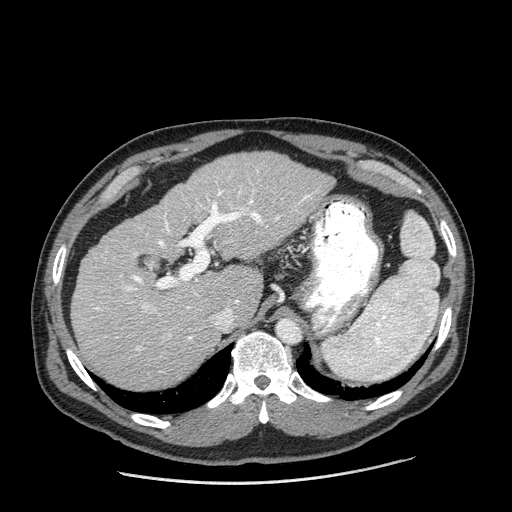
Contrast-enhanced abdominal CT (liver protocol), one axial slice. Slice 129 of 198 in the series (ordered by position). Reconstruction kernel STANDARD. One of 2 acquisitions stored at this slice position. Soft-tissue window (W 400 / L 40 HU). 512 × 512 image matrix, field of view 400 × 400 mm. Case-level facts recorded for this patient, not image findings: diagnosis: hepatocellular carcinoma (patient treated with transarterial chemoembolisation; whether this scan precedes or follows treatment is not stated here); TNM stage (as recorded): Stage-II; Child-Pugh class: A; tumour differentiation: moderately differentiated; tumour size: 2.6 cm.
Annotated regions visible in this slice (semi-automatically segmented with operator editing):
- liver parenchyma outside the tumour (the mass and vessels are separate outlines, so this box may not span the whole liver): box from (x=70, y=152) to (x=334, y=390) px
- liver vessels: (x=96, y=170)–(x=311, y=351)